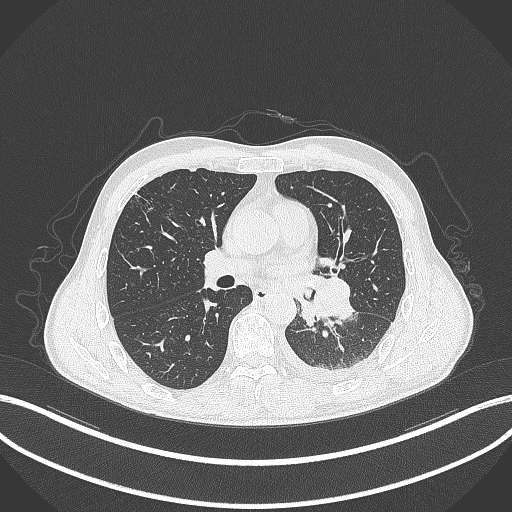
Chest CT, one axial slice. Slice 173 of 295 in the series (ordered by position). Reconstruction kernel B70f. Lung window (W 1500 / L -600 HU). 1 mm slice thickness. 512 × 512 image matrix, field of view 400 × 400 mm. Patient: male, 47 years. From the clinical record (not read from this slice): clinical TNM (as recorded): T3 N1 M1c; histopathological grade: G3.
Annotated regions visible in this slice (bounding box drawn by a radiologist):
- lung tumour (recorded histology: small cell carcinoma): bounding box [x1, y1, x2, y2] px = [296, 275, 357, 327]